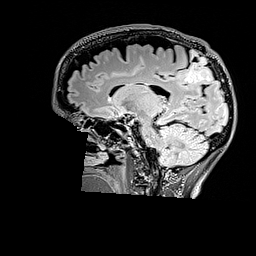
Brain MRI from a brain-tumour surgery series, one sagittal slice; position 103 of 176 along the scan axis; T2 FLAIR; 256 × 256 image matrix, field of view 256 × 256 mm. From the clinical record (not read from this slice): histopathology: Astrocytoma; WHO grade: 3; IDH mutation: yes; tumour location: Right Parietal.
Structures marked on this image (expert manual segmentation):
- tumour: bounding box <185,50,212,82> (left, top, right, bottom; pixels)
- tumour: <186,57,214,83>